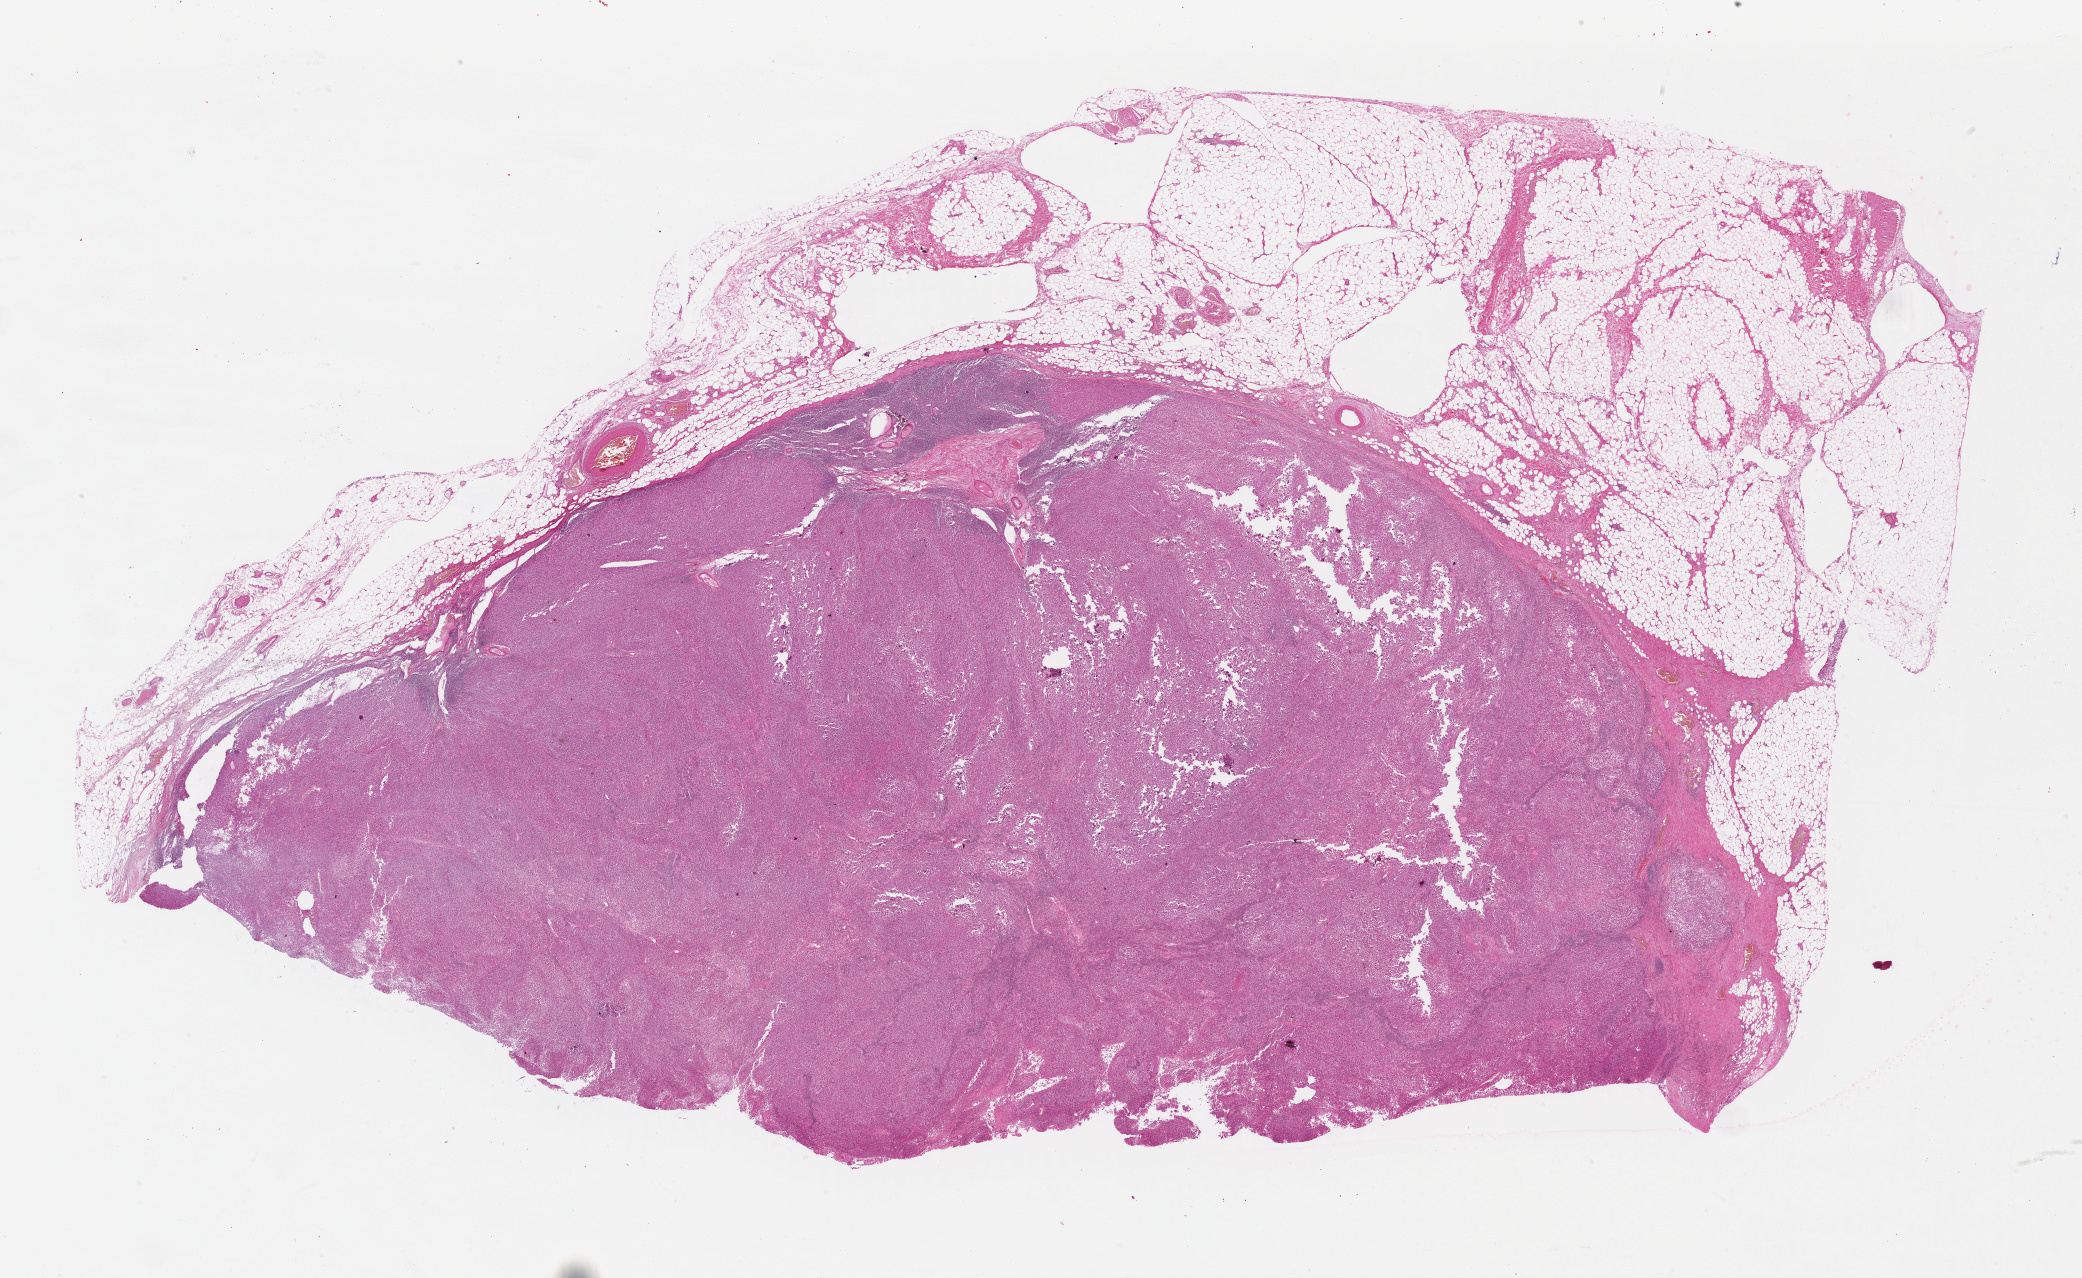
Whole-slide histology image, H&E — low-resolution overview of the scanned area, about 32.7 x 20.1 mm (slide scanned at 40x), formalin-fixed paraffin-embedded (FFPE) diagnostic section, skin, primary tumour sample. Male patient; age at initial diagnosis 45 years.
Diagnosis: Malignant melanoma, NOS.